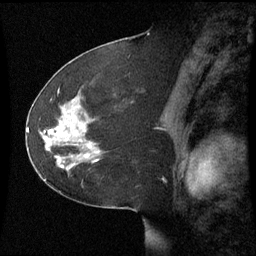
Breast MRI (dynamic contrast-enhanced), one sagittal slice; position 34 of 60 along the scan axis; dynamic contrast-enhanced series, image 2 of 3 at this slice position (ordered by acquisition); 1.5 T; TE 4.2 ms, TR 8.9 ms; 2.2 mm slice thickness; 256 × 256 image matrix, field of view 220 × 220 mm. Patient: female, 51 years. Case-level facts recorded for this patient, not image findings: setting: breast cancer imaged before/during neoadjuvant chemotherapy; receptor status: HR-positive, HER2-negative.
Structures marked on this image (semi-automatic segmentation, software-assisted and operator-edited):
- analysis volume of interest (the breast-tissue region the enhancement analysis was run in; not a lesion): bounding box (x1, y1, x2, y2) in pixels: (44, 102, 103, 169)
- tumour enhancement mask (voxels above the 70 % enhancement threshold inside the analysis volume of interest): (88, 146, 91, 149)